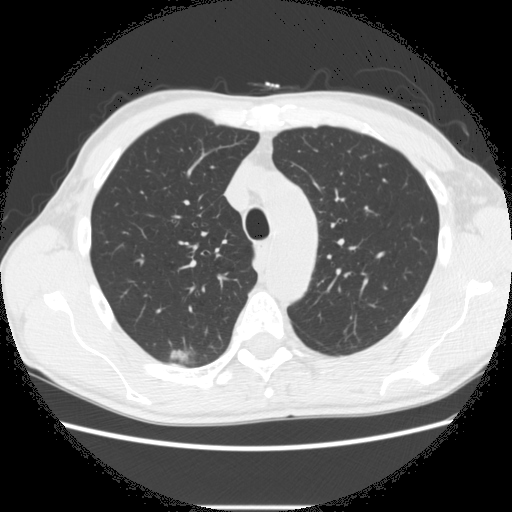
Low-dose screening chest CT, one axial slice; position 210 of 282 along the scan axis; lung window (W 1500 / L -600 HU); 512 × 512 image matrix, field of view 360 × 360 mm.
Structures marked on this image (manually delineated by an expert):
- lesion 1 (tumor, upper lobe of right lung): bounding box [x1, y1, x2, y2] px = [170, 349, 189, 363]